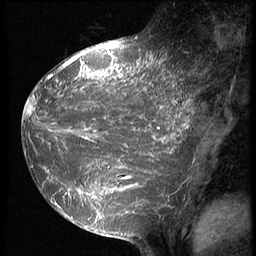
Breast MRI (dynamic contrast-enhanced), one sagittal slice. Position 25 of 64 along the scan axis. 3 images stored at this slice position (order not interpretable as contrast timing). 1.5 T. TE 4.2 ms, TR 9 ms. 256 × 256 image matrix, field of view 180 × 180 mm. Patient: female, 39 years. Case-level facts recorded for this patient, not image findings: setting: breast cancer imaged before/during neoadjuvant chemotherapy; receptor status: HER2-positive.
Outlined on this slice (semi-automatically segmented with operator editing):
- analysis volume of interest (the breast-tissue region the enhancement analysis was run in; not a lesion): box from (x=23, y=47) to (x=199, y=239) px
- tumour enhancement mask (voxels above the 140 % enhancement threshold inside the analysis volume of interest): (x=23, y=47)–(x=195, y=223)